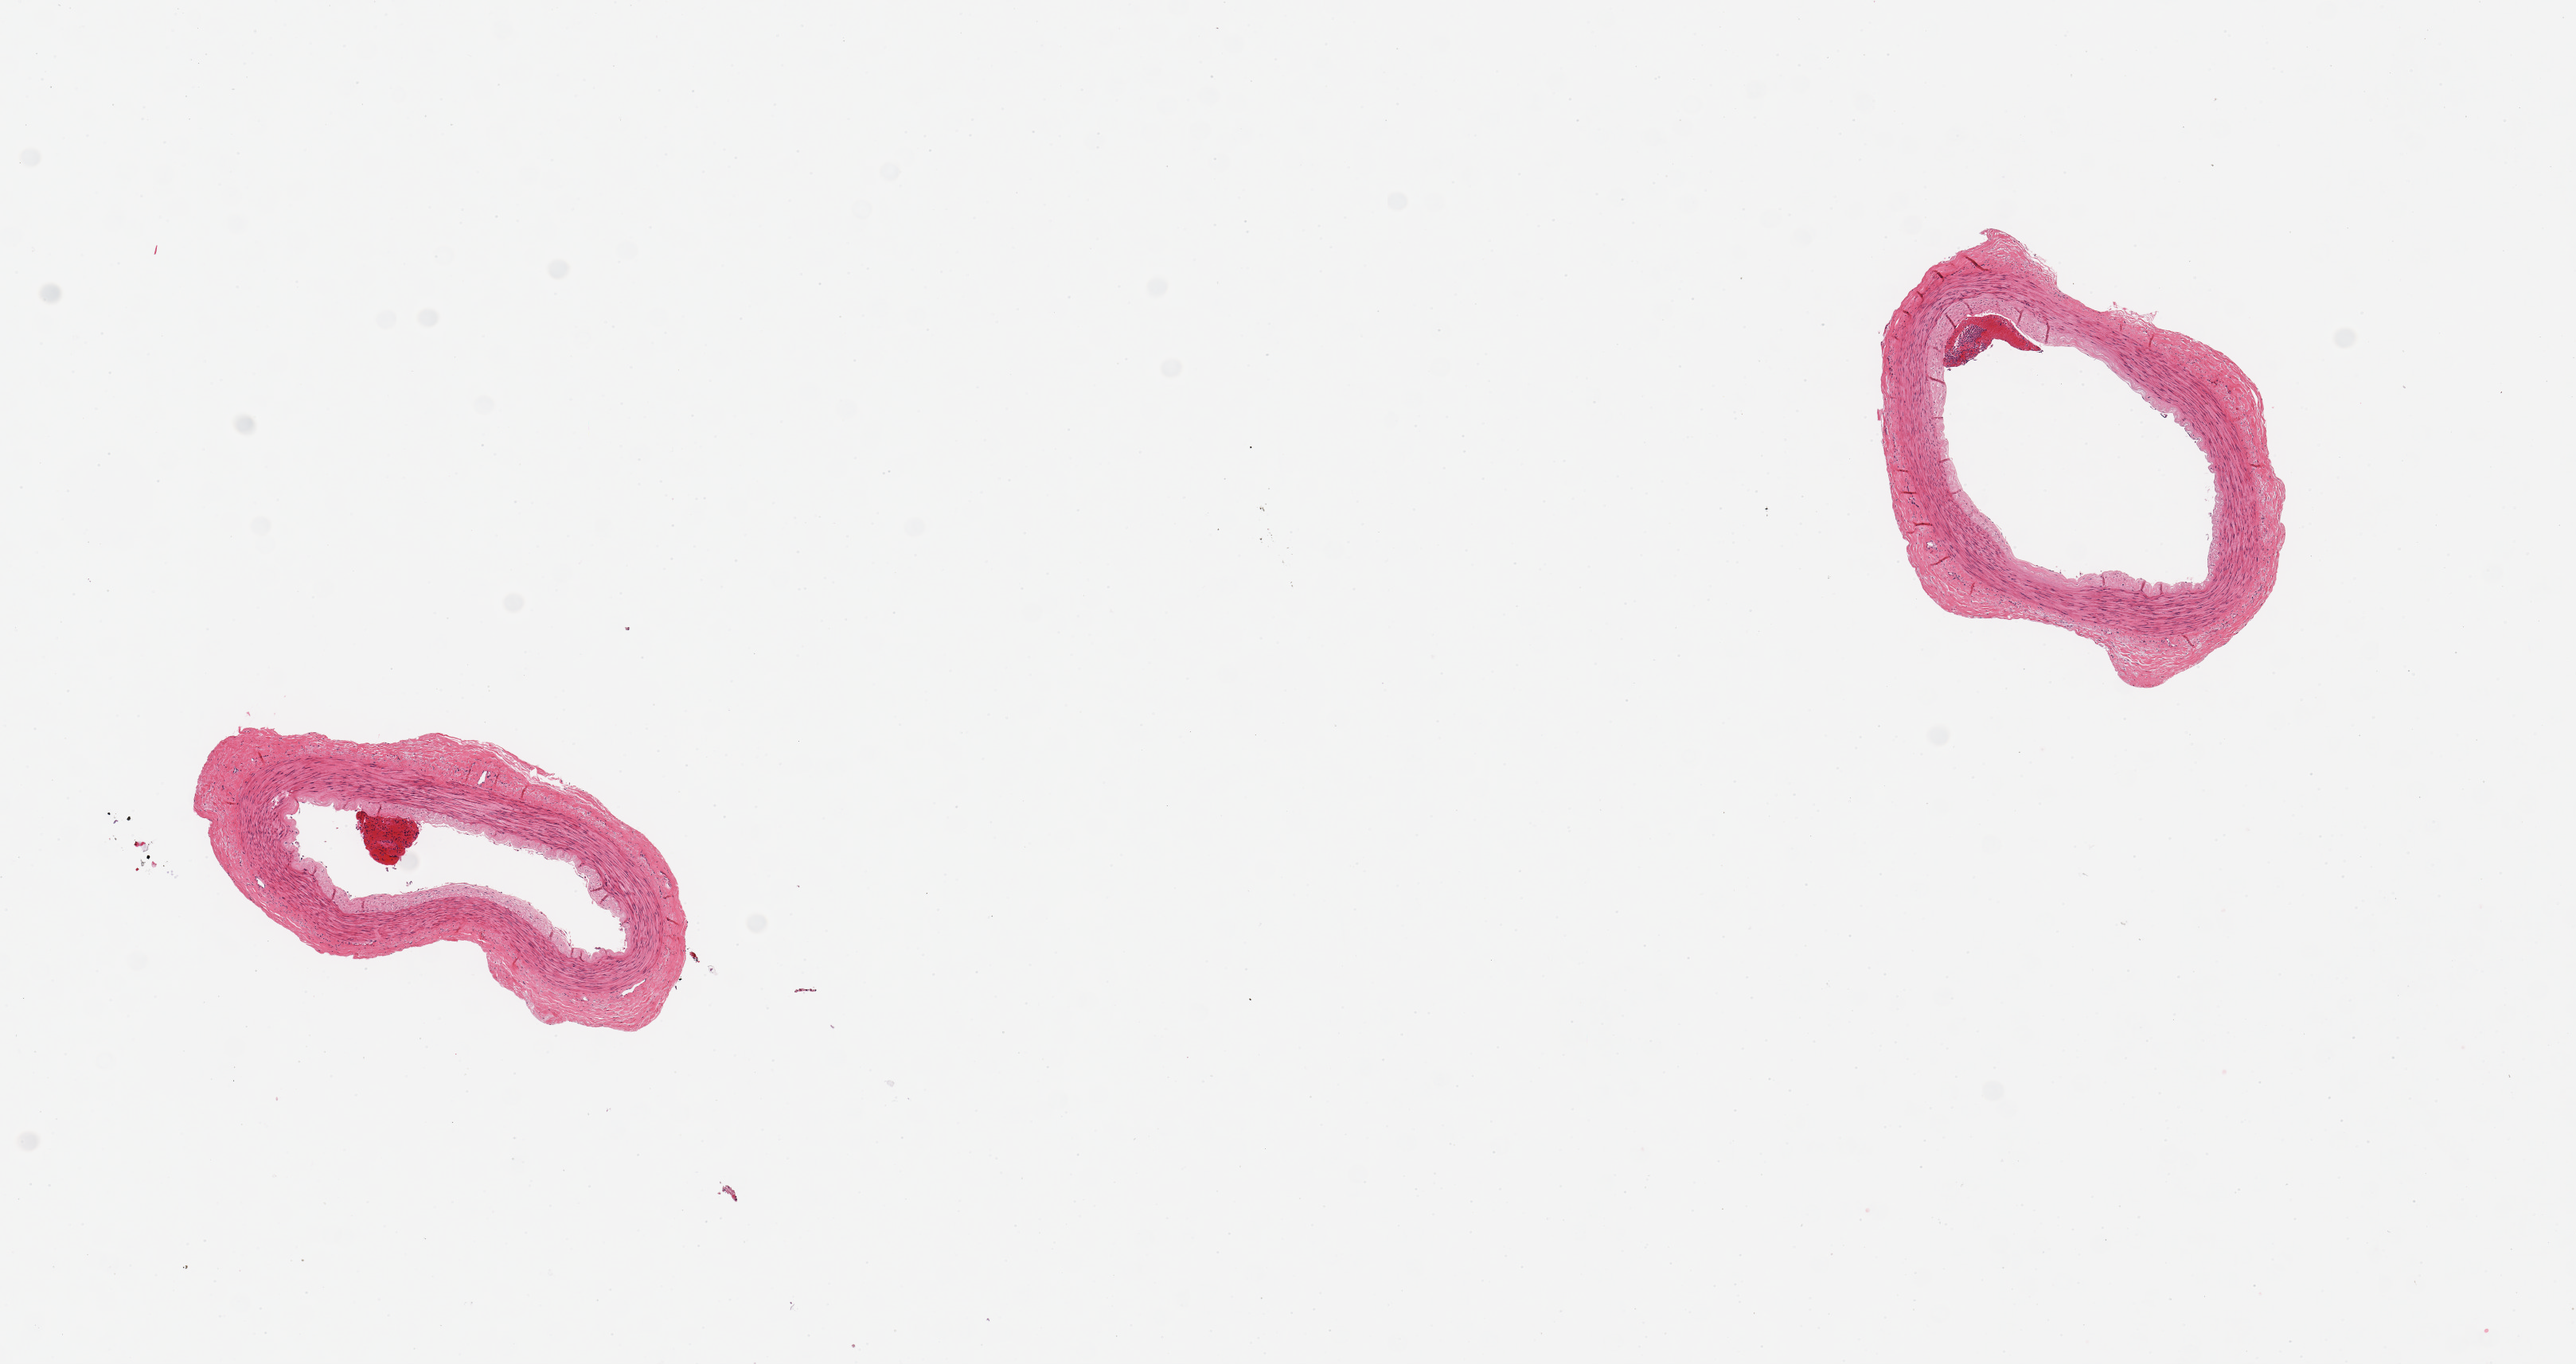
H&E whole-slide image — low-resolution overview of the scanned area, about 12.8 x 6.8 mm (acquisition: 20x scan), PAXgene-fixed, paraffin-embedded tissue, sampled site (target tissue): tibial artery, tissue donor sample. Donor sex: female.
* review note (as recorded): 2 pieces; well dissected; no plaques; small, 0.4 mm, adherent blood clot